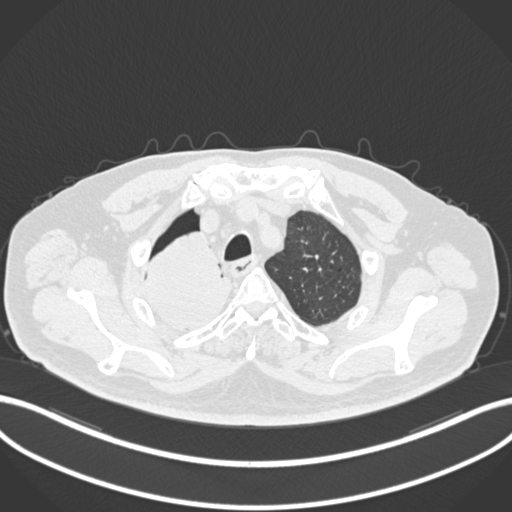
Chest CT, one axial slice. Slice 178 of 218 in the series (ordered by position). Reconstruction kernel B30f. 120 kVp. Lung window (W 1500 / L -600 HU). 1 mm slice thickness. 512 × 512 image matrix. Patient: male, 68 years. Case-level facts recorded for this patient, not image findings: clinical TNM (as recorded): T2a N0 M0.
Outlined on this slice (rectangle marked by the reading radiologist):
- lung tumour (recorded histology: adenocarcinoma): bounding box (x1, y1, x2, y2) in pixels: (144, 235, 232, 330)